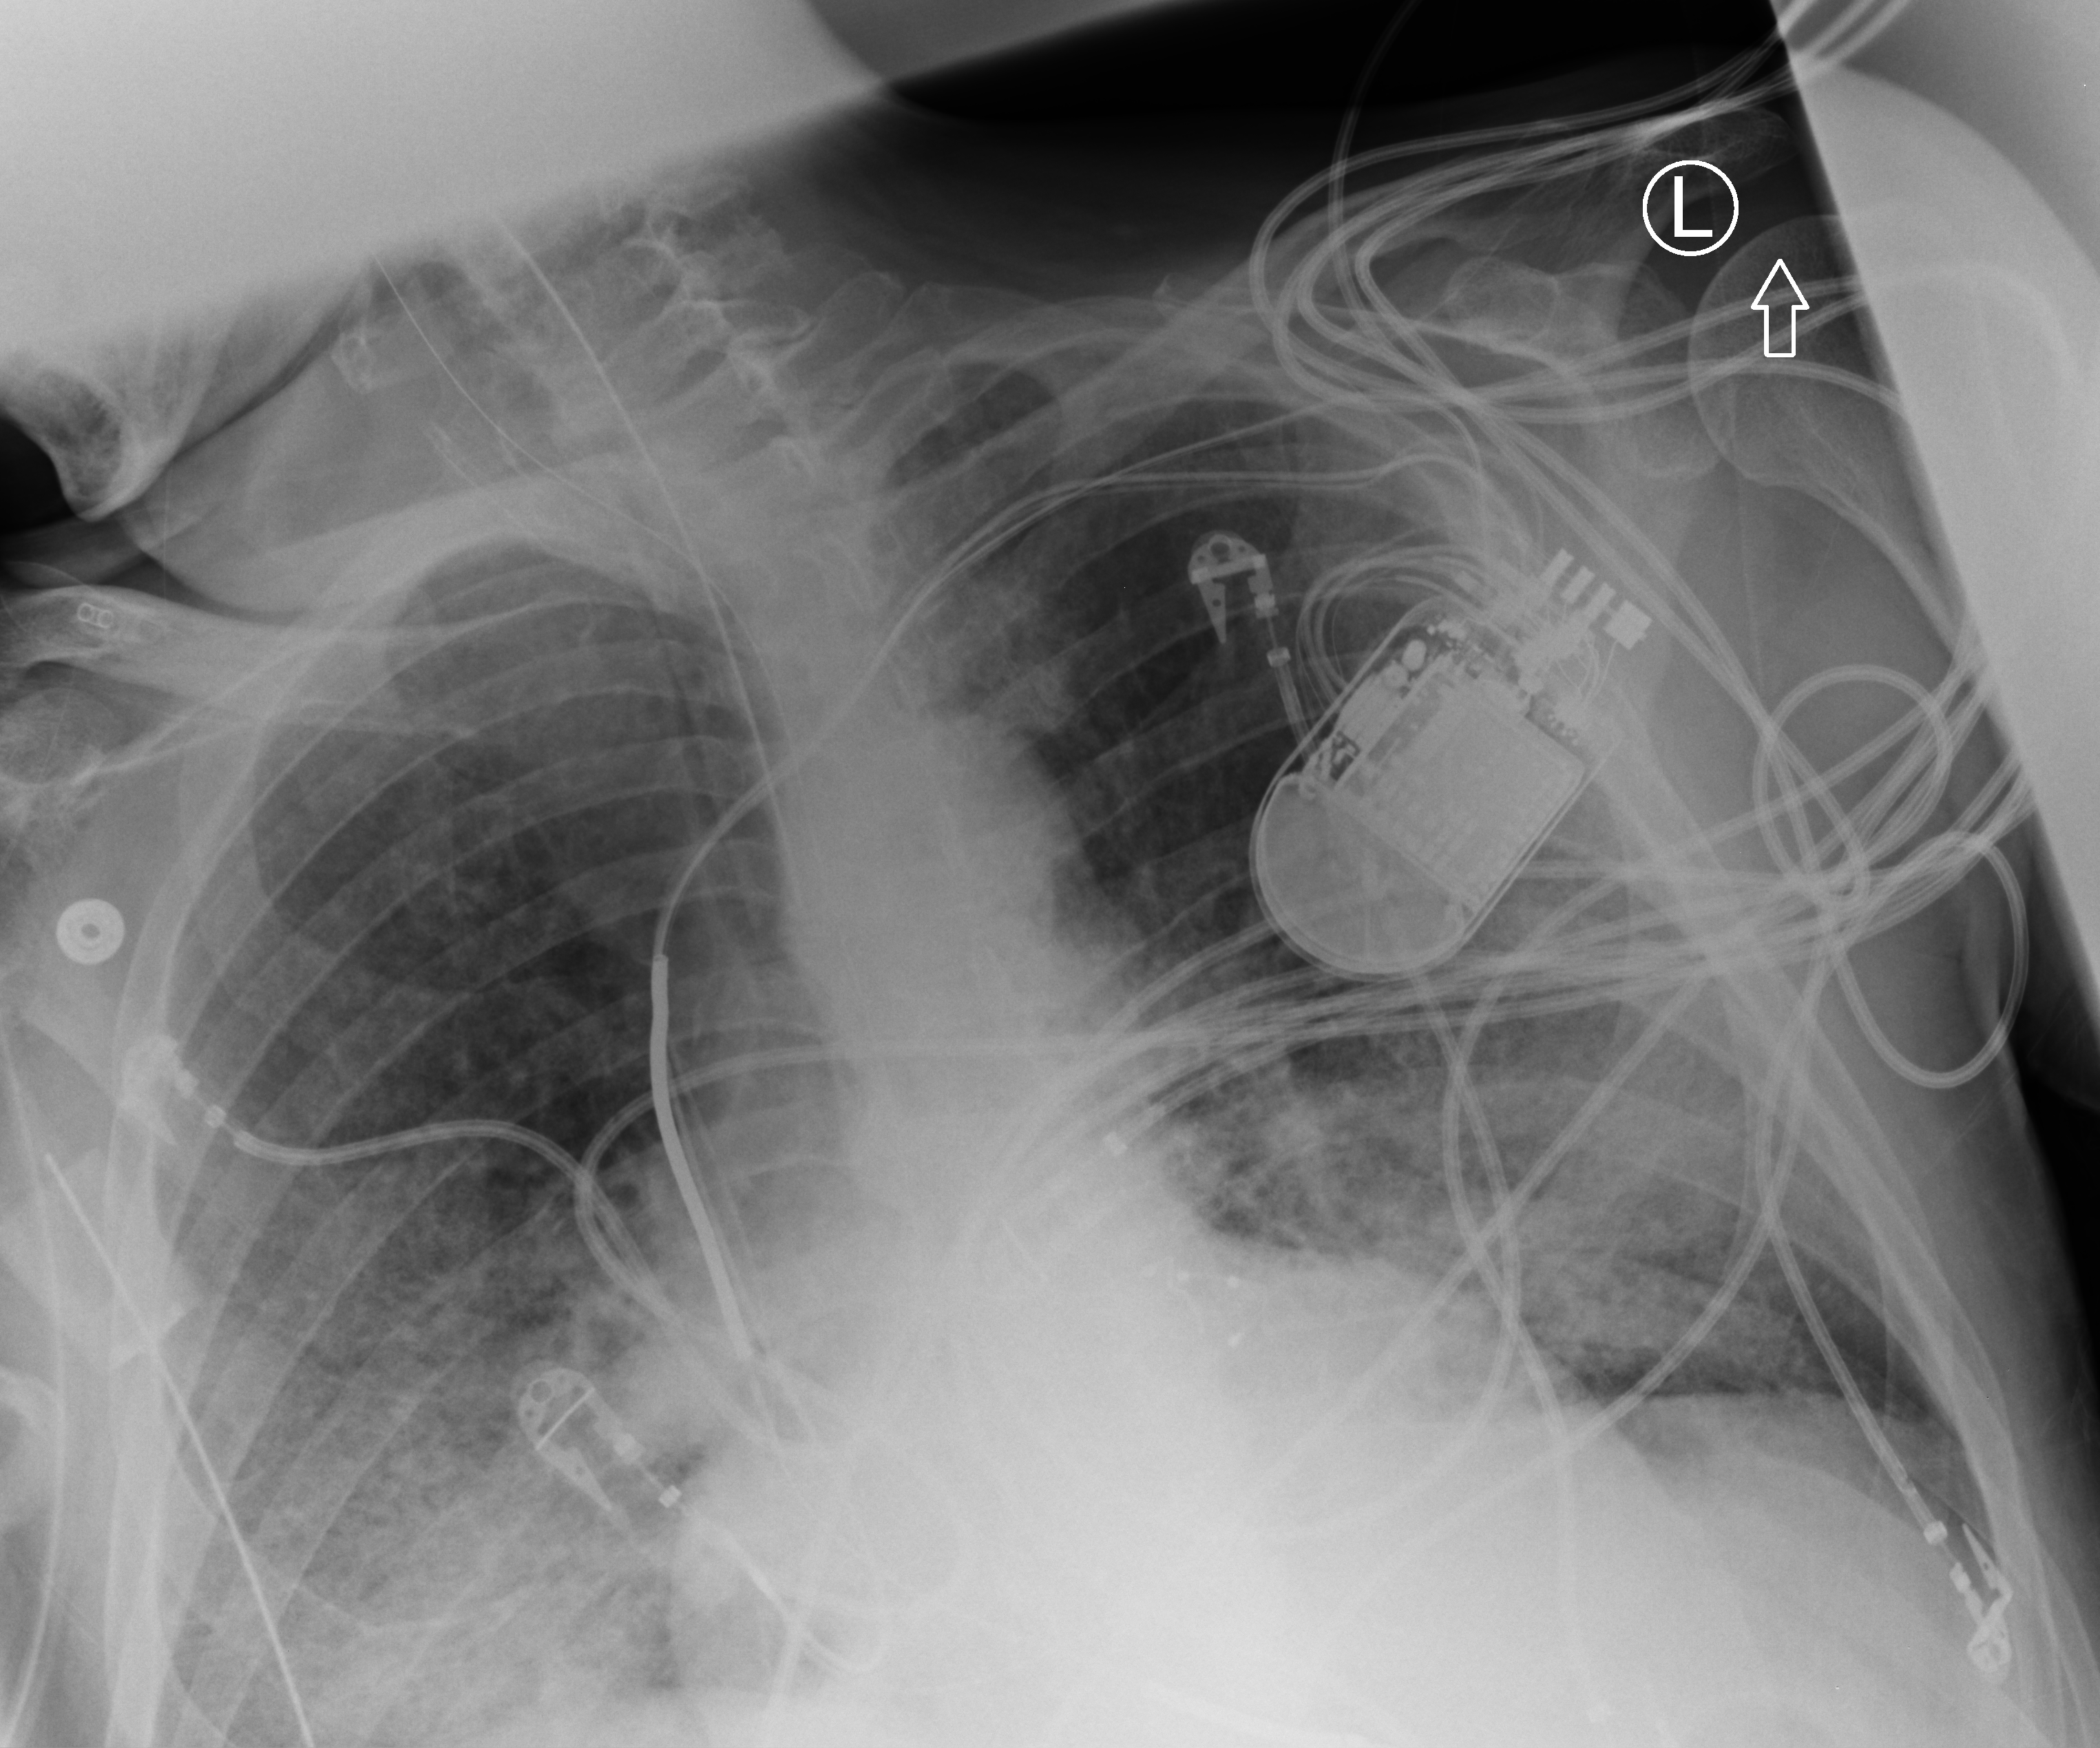
Bedside chest radiograph (computed radiography). Male patient hospitalised with COVID-19, age 60–74 years.
Admission-level facts for this patient (not findings on this image; timing relative to this image not recorded): COPD (admission record): no.